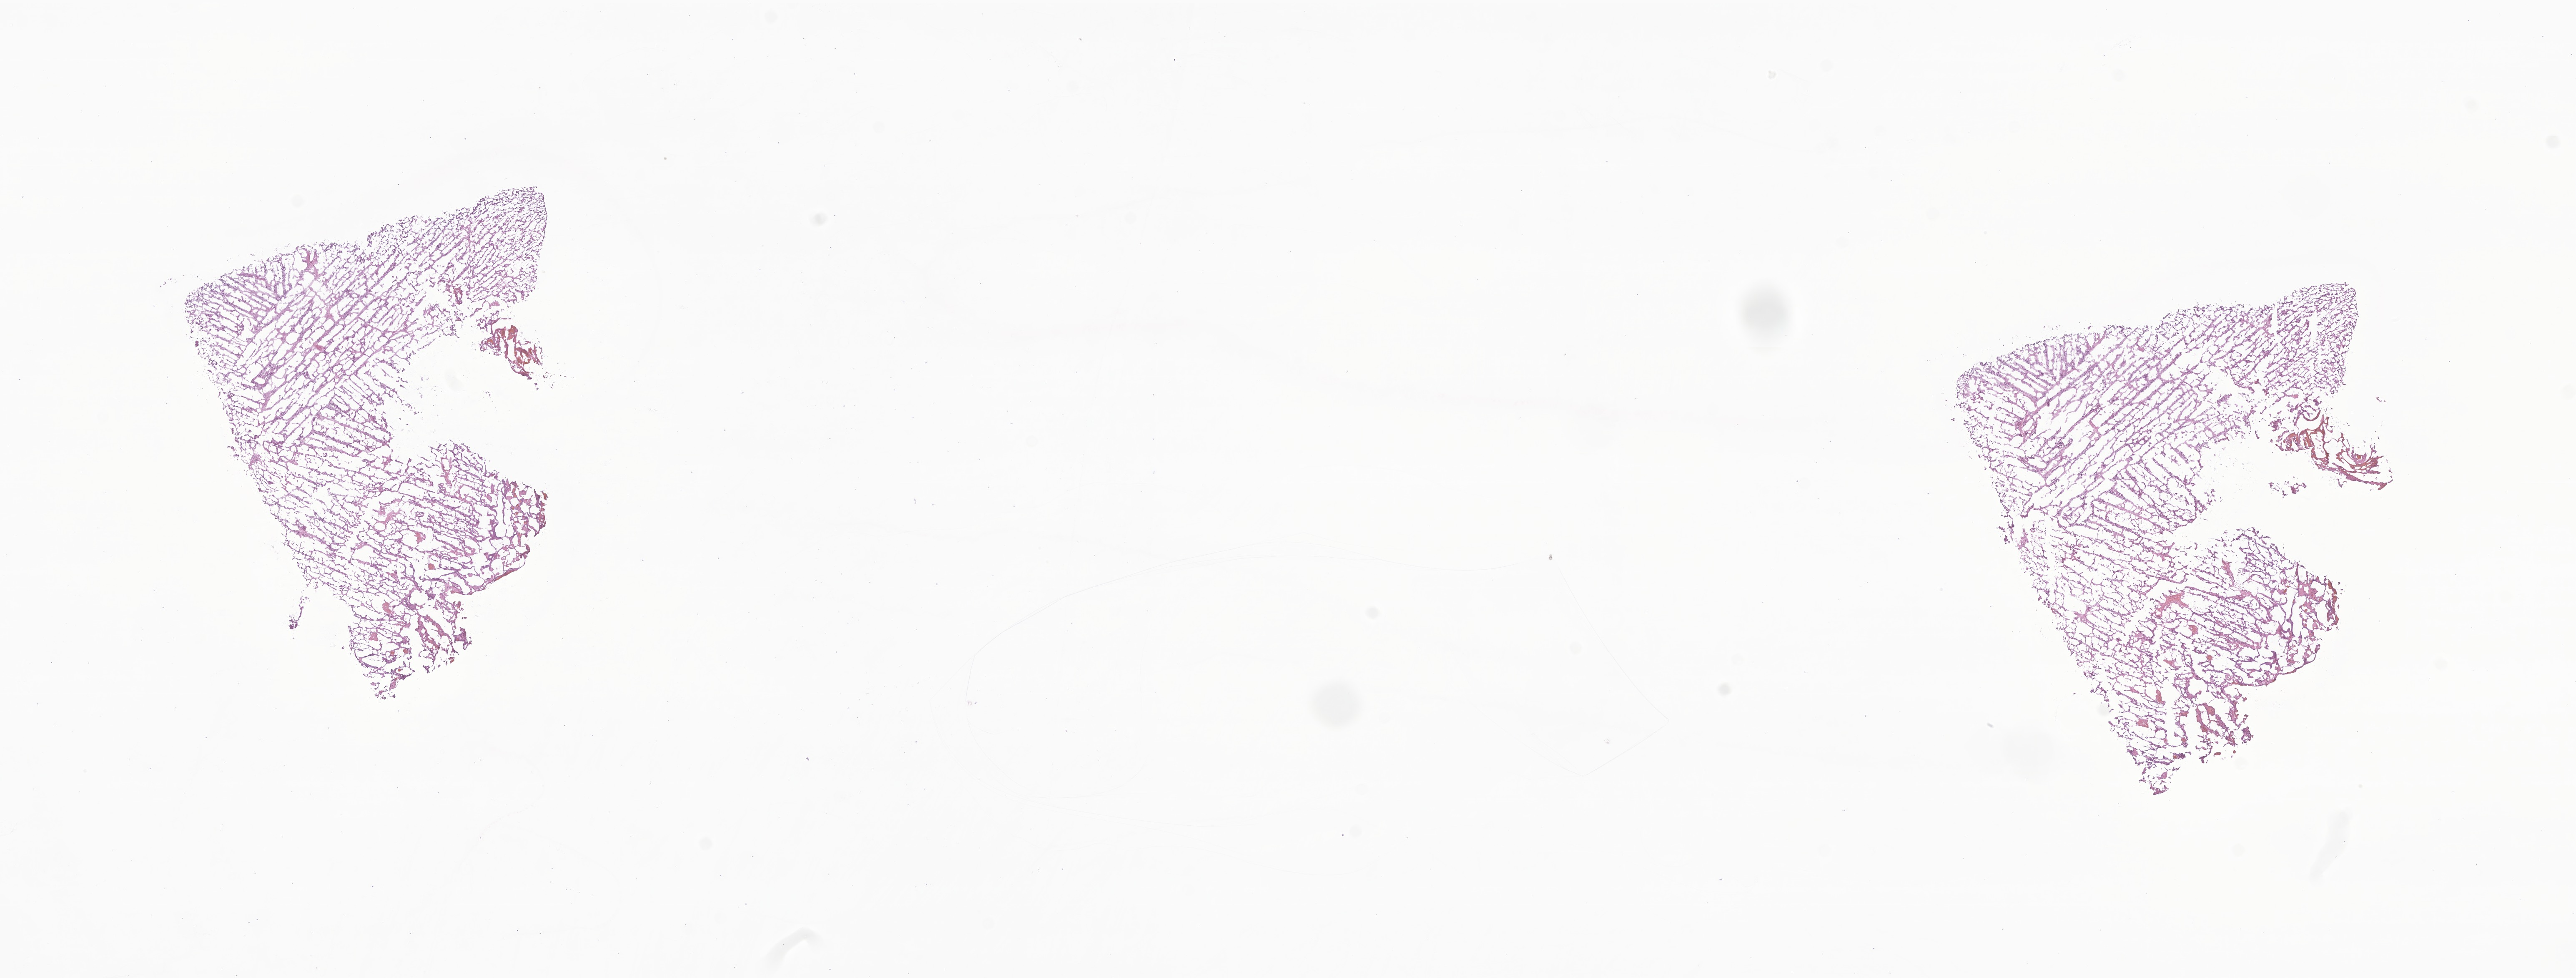
Digitized hematoxylin and eosin (H&E)-stained section of tumor tissue from the cerebral ventricle — low-resolution overview of the scanned area, about 26.0 x 9.9 mm; frozen section. Male patient, age 183 months (15 years 3 months).
Diagnosis (ICD-O-3 morphology term): Ependymoma, NOS.